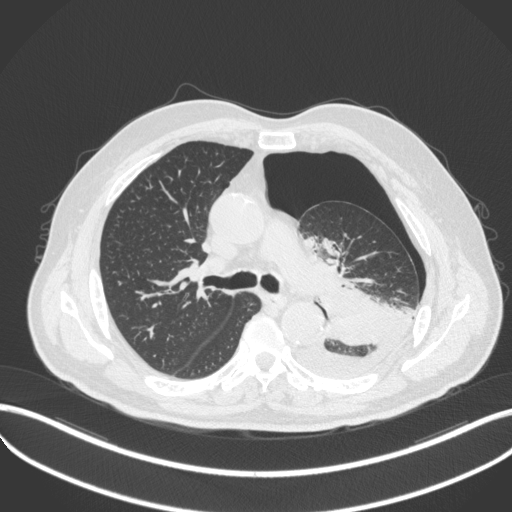
Chest CT, one axial slice. Position 329 of 466 along the scan axis. Reconstruction kernel B31f. 120 kVp. Lung window (W 1500 / L -600 HU). 1 mm slice thickness. 512 × 512 image matrix, field of view 400 × 400 mm. Patient: male, 76 years. Case-level facts recorded for this patient, not image findings: clinical TNM (as recorded): T3 N0 M1b.
Outlined on this slice (rectangle marked by the reading radiologist):
- lung tumour (recorded histology: adenocarcinoma): bounding box [x1, y1, x2, y2] px = [313, 277, 405, 350]